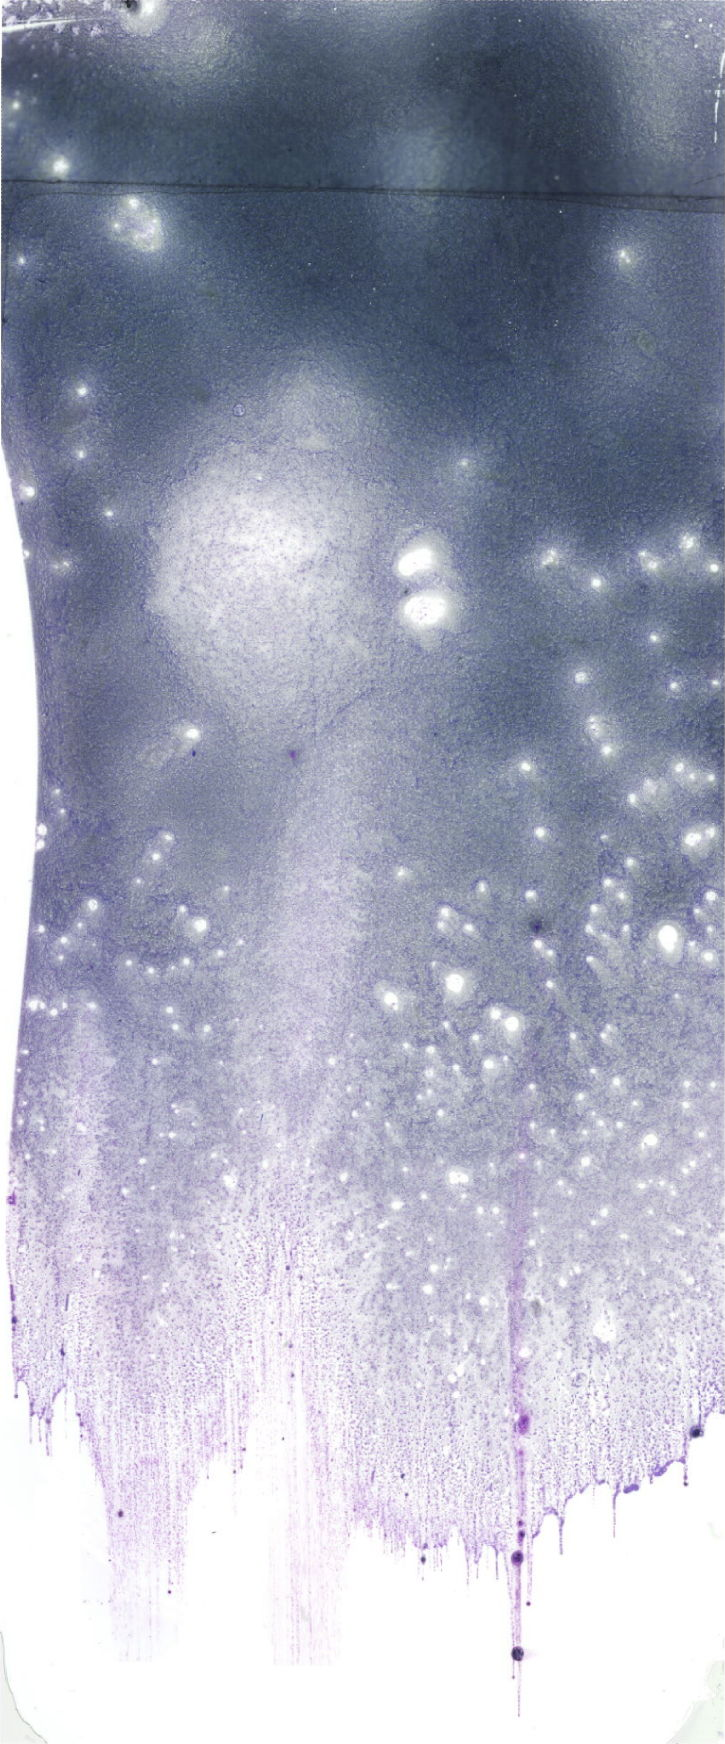
May-Grünwald–Giemsa-stained marrow aspirate smear (whole slide), a low-resolution overview of the entire scanned area, about 20.6 x 49.4 mm. Male patient.
Diagnosis: Acute Erythroid Leukemia.